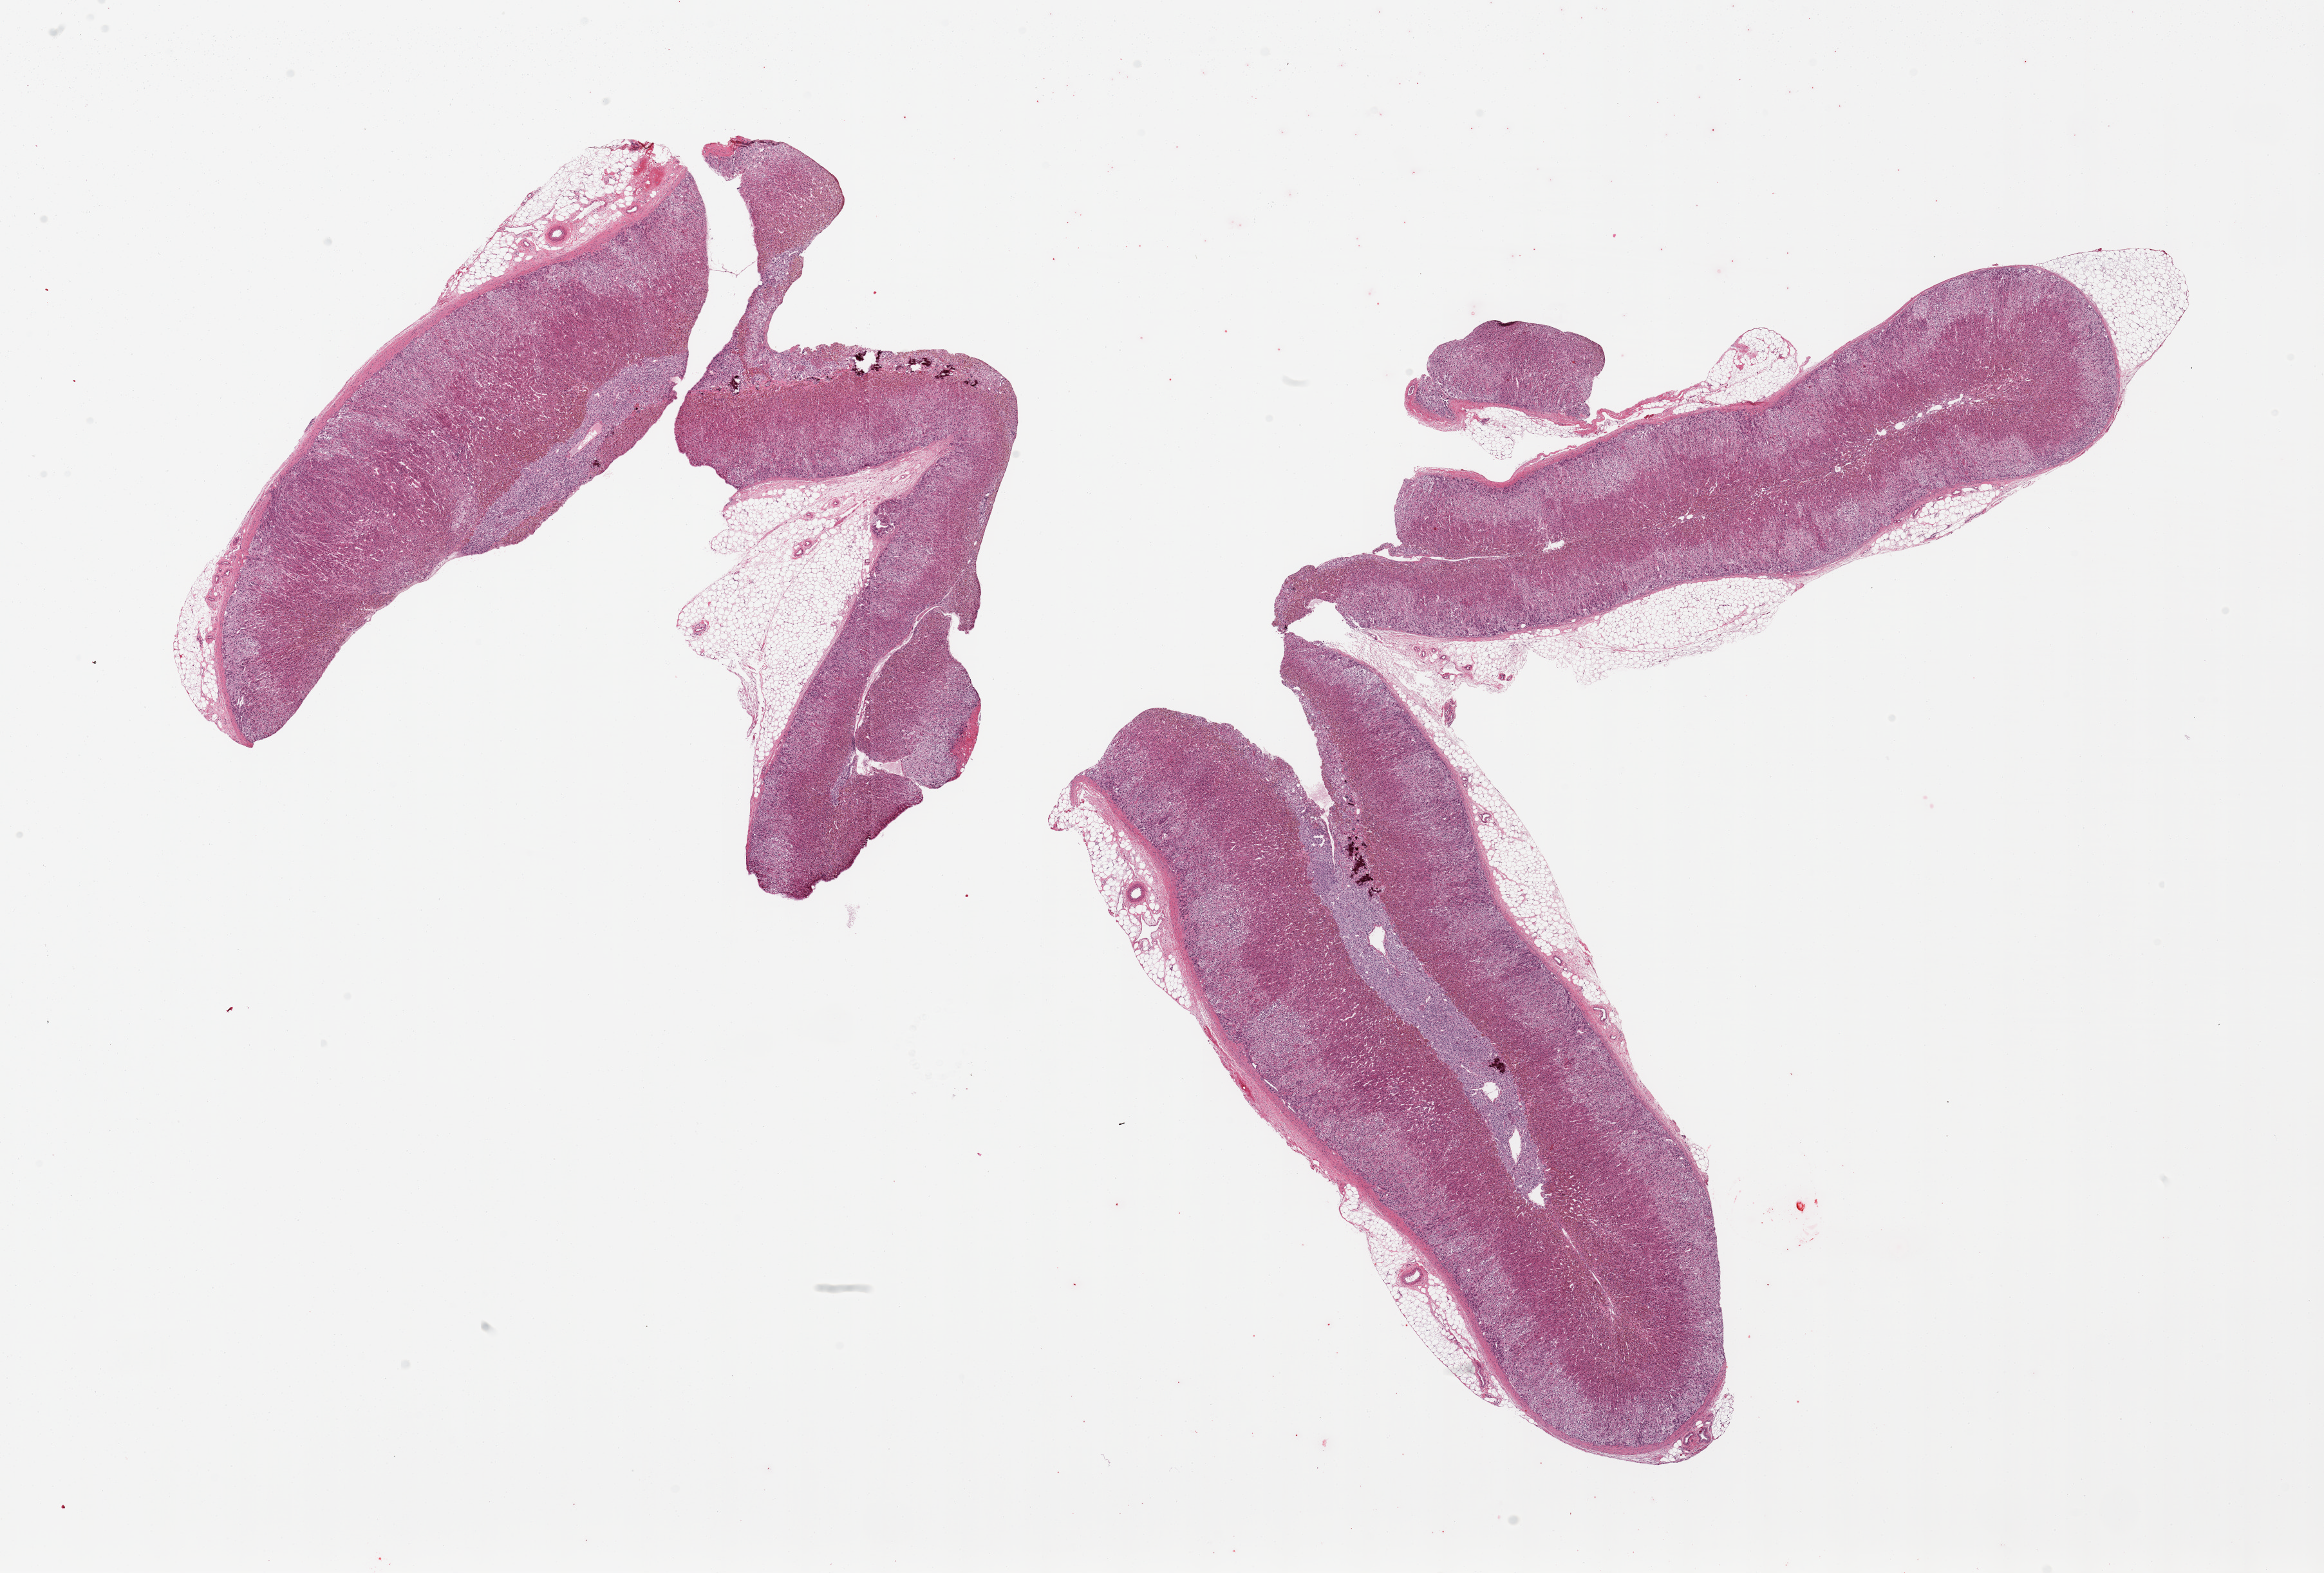
Digitized H&E-stained section — whole scanned area (about 28.5 x 19.3 mm) shown as a low-resolution overview, PAXgene-fixed, paraffin-embedded tissue, sampled site (target tissue): adrenal gland, tissue donor sample. Male donor.
• pathologist's review note for this sample: 2 pieces; includes ~10 and 20% attached fat, cortex and medulla, focal calcification